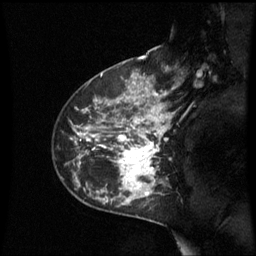
Breast MRI (dynamic contrast-enhanced), one sagittal slice. Position 41 of 60 along the scan axis. Dynamic contrast-enhanced series, image 2 of 3 at this slice position (ordered by acquisition). 1.5 T. TE 4.2 ms, TR 8.9 ms. 256 × 256 image matrix, field of view 210 × 210 mm. Patient: female, 42 years. From the clinical record (not read from this slice): setting: breast cancer imaged before/during neoadjuvant chemotherapy; receptor status: HER2-positive.
Structures marked on this image (semi-automatically segmented with operator editing):
- analysis volume of interest (the breast-tissue region the enhancement analysis was run in; not a lesion): bounding box [x1, y1, x2, y2] px = [62, 93, 171, 210]
- tumour enhancement mask (voxels above the 70 % enhancement threshold inside the analysis volume of interest): [79, 93, 171, 196]